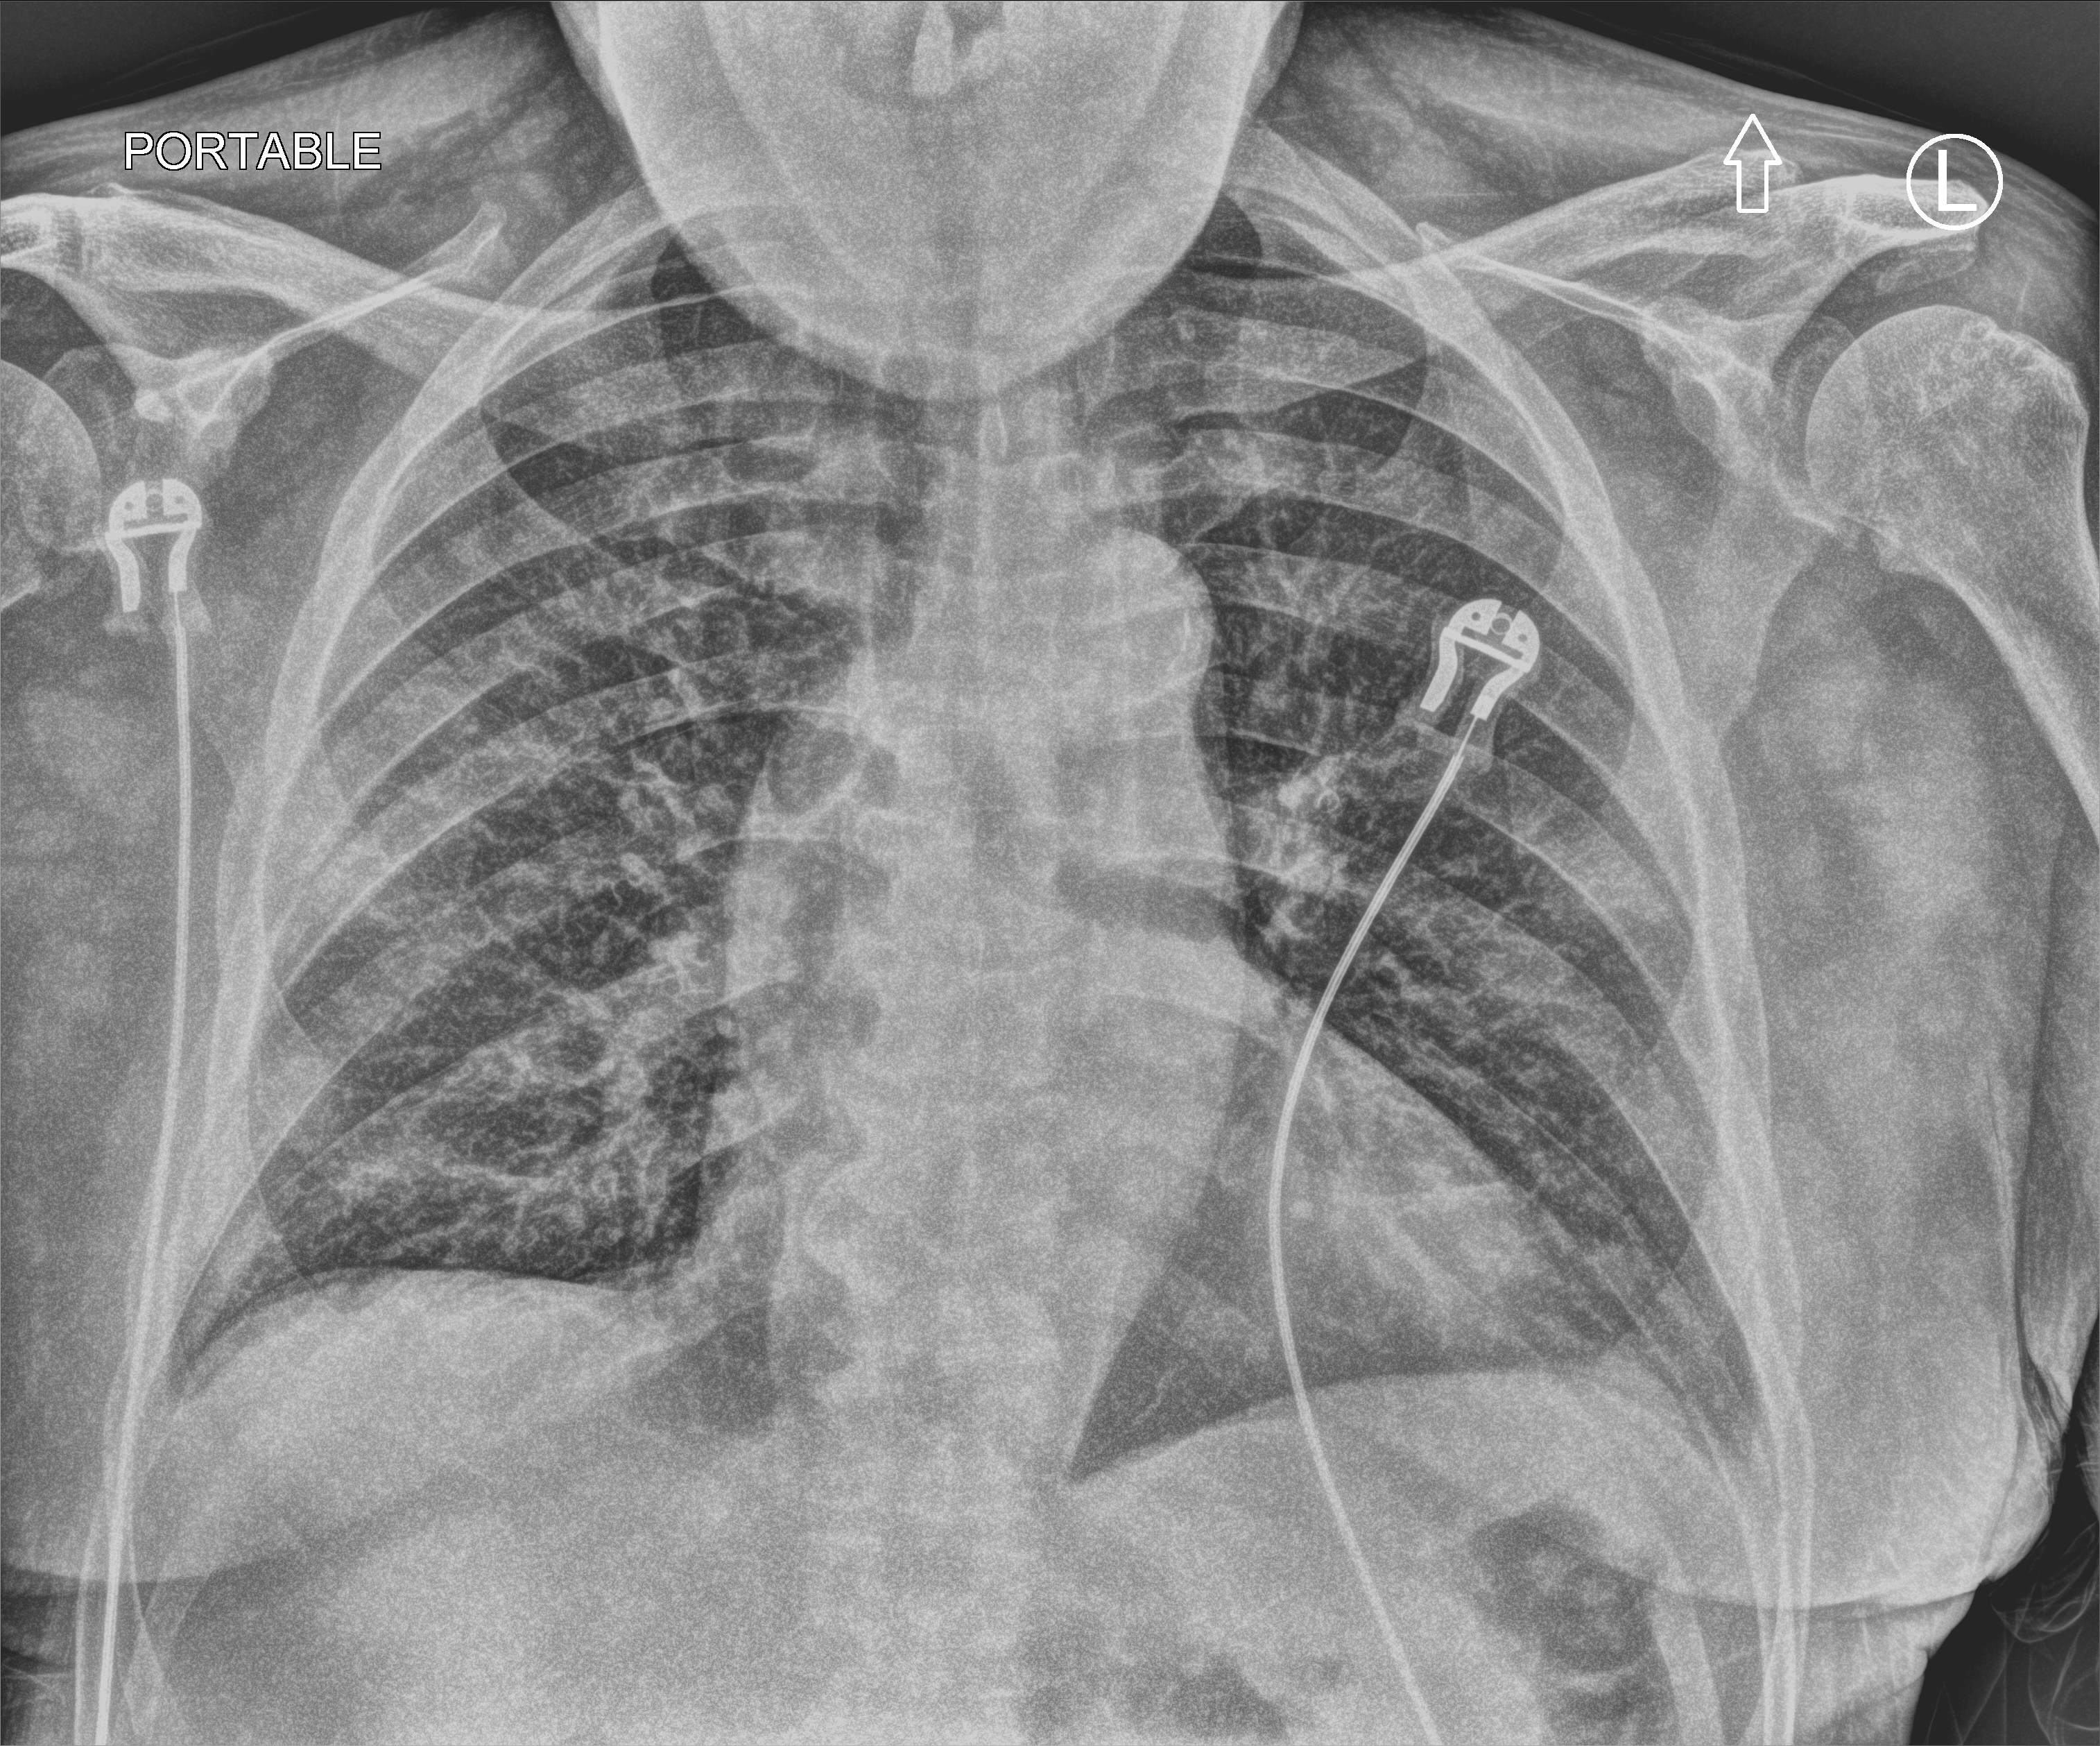
Chest X-ray (portable), anteroposterior (AP) projection. Male patient hospitalised with COVID-19, age 60–74 years.
From the hospital-stay record, not from the radiograph (when in the stay this image was taken is not recorded): mechanically ventilated during this hospital stay: no; smoking status (admission record): never; length of hospital stay: 4 days.